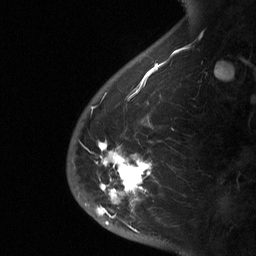
Breast MRI (dynamic contrast-enhanced), one sagittal slice. Position 14 of 64 along the scan axis. Dynamic contrast-enhanced study with each time point stored as its own series, time point 2 of 3 at this slice position (early post-contrast, ordered by acquisition time). 1.5 T. TE 4.8 ms, TR 27 ms. 256 × 256 image matrix, field of view 180 × 180 mm. Female patient, age 56 years. Case-level facts recorded for this patient, not image findings: setting: breast cancer imaged before/during neoadjuvant chemotherapy; receptor status: HER2-positive.
Outlined on this slice (semi-automatically segmented with operator editing):
- analysis volume of interest (the breast-tissue region the enhancement analysis was run in; not a lesion): bounding box <66,138,182,229> (left, top, right, bottom; pixels)
- tumour enhancement mask (voxels above the 90 % enhancement threshold inside the analysis volume of interest): <96,141,152,228>